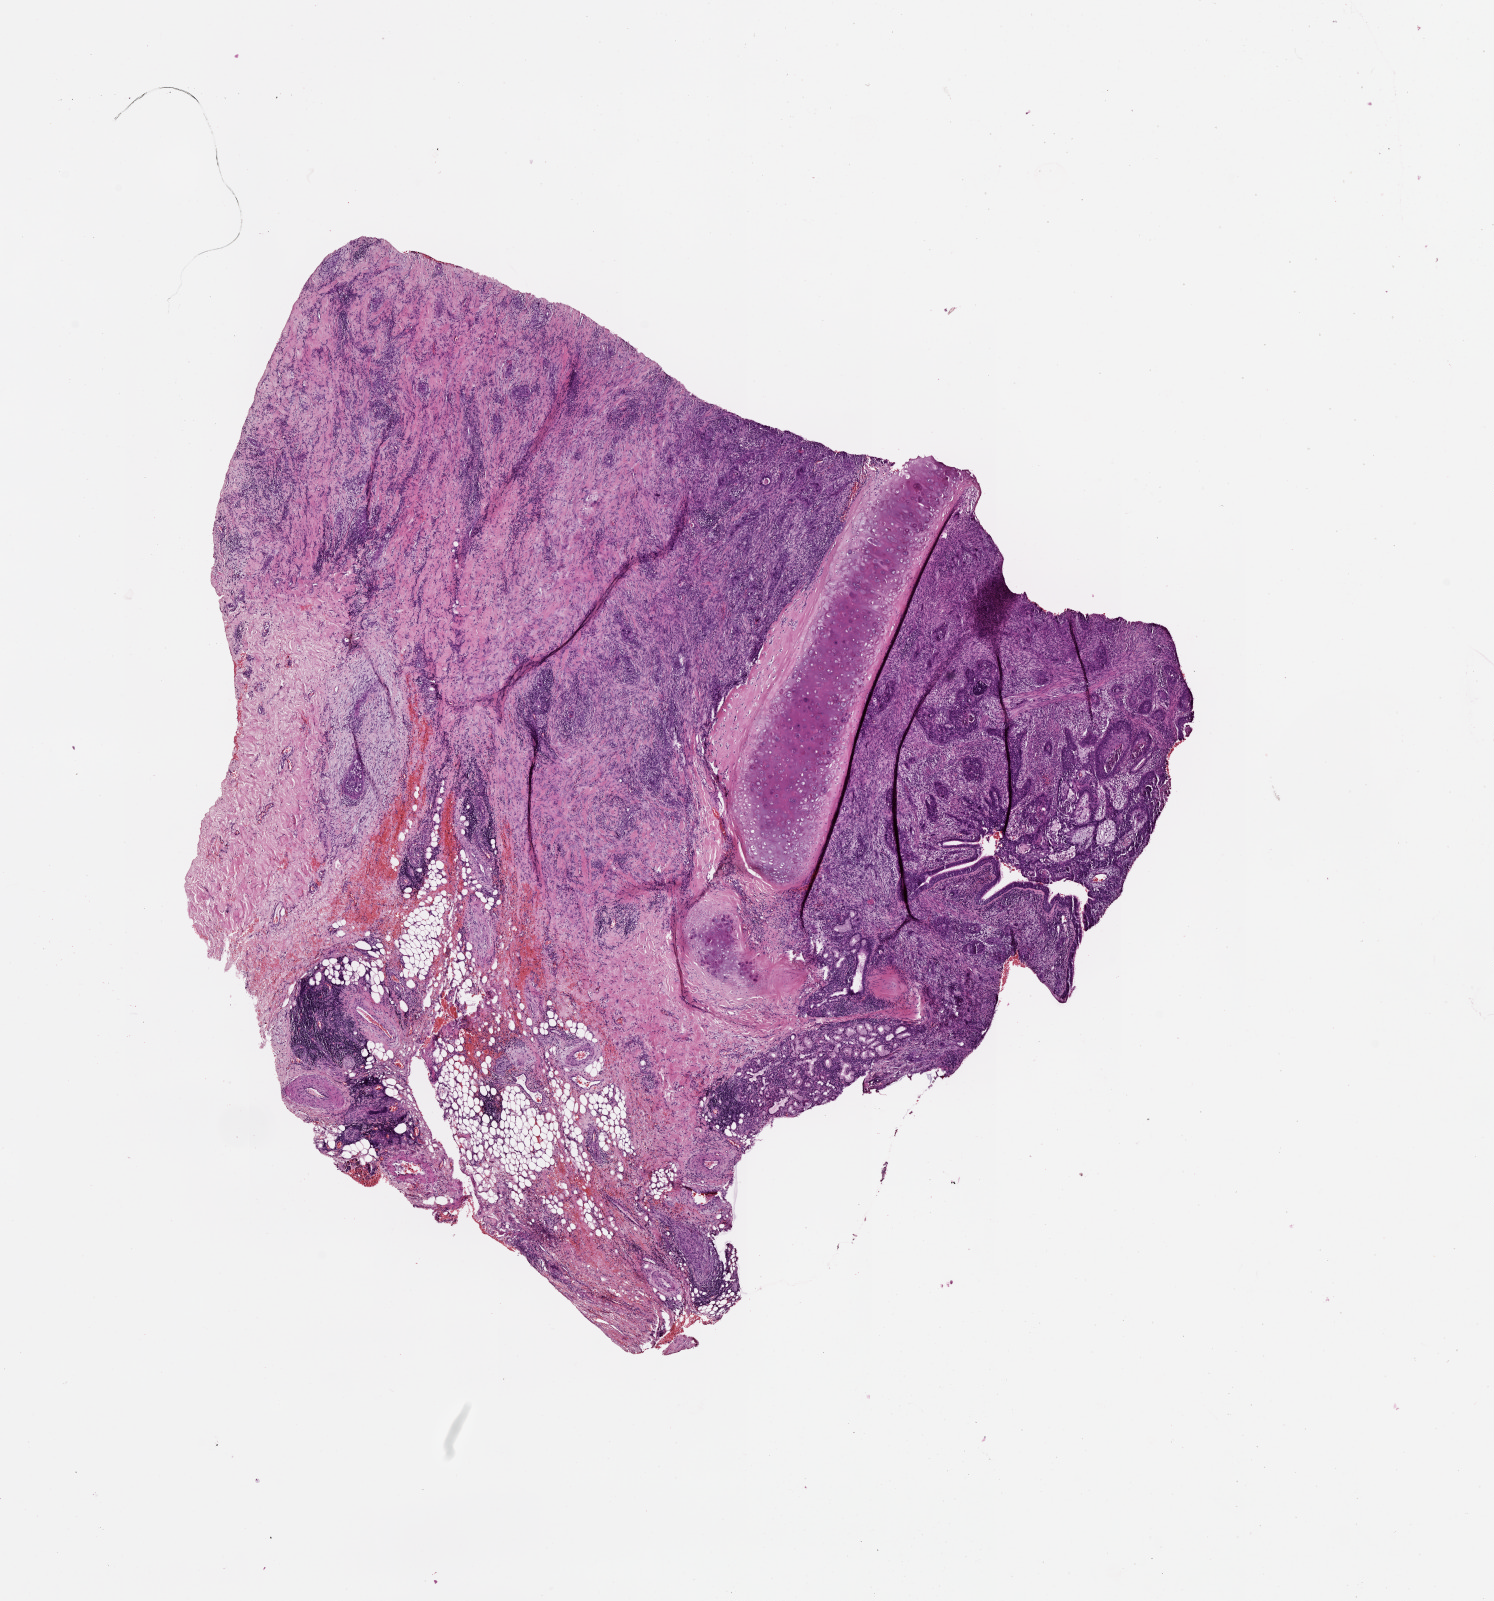
Digitized H&E tissue section (whole slide) — whole scanned area (about 12.0 x 12.9 mm, from a 20x scan) shown as a low-resolution overview. Tumour tissue sample, lung. Female, 56 y/o.
- patient diagnosis (cohort enrolment): squamous cell carcinoma (lung)